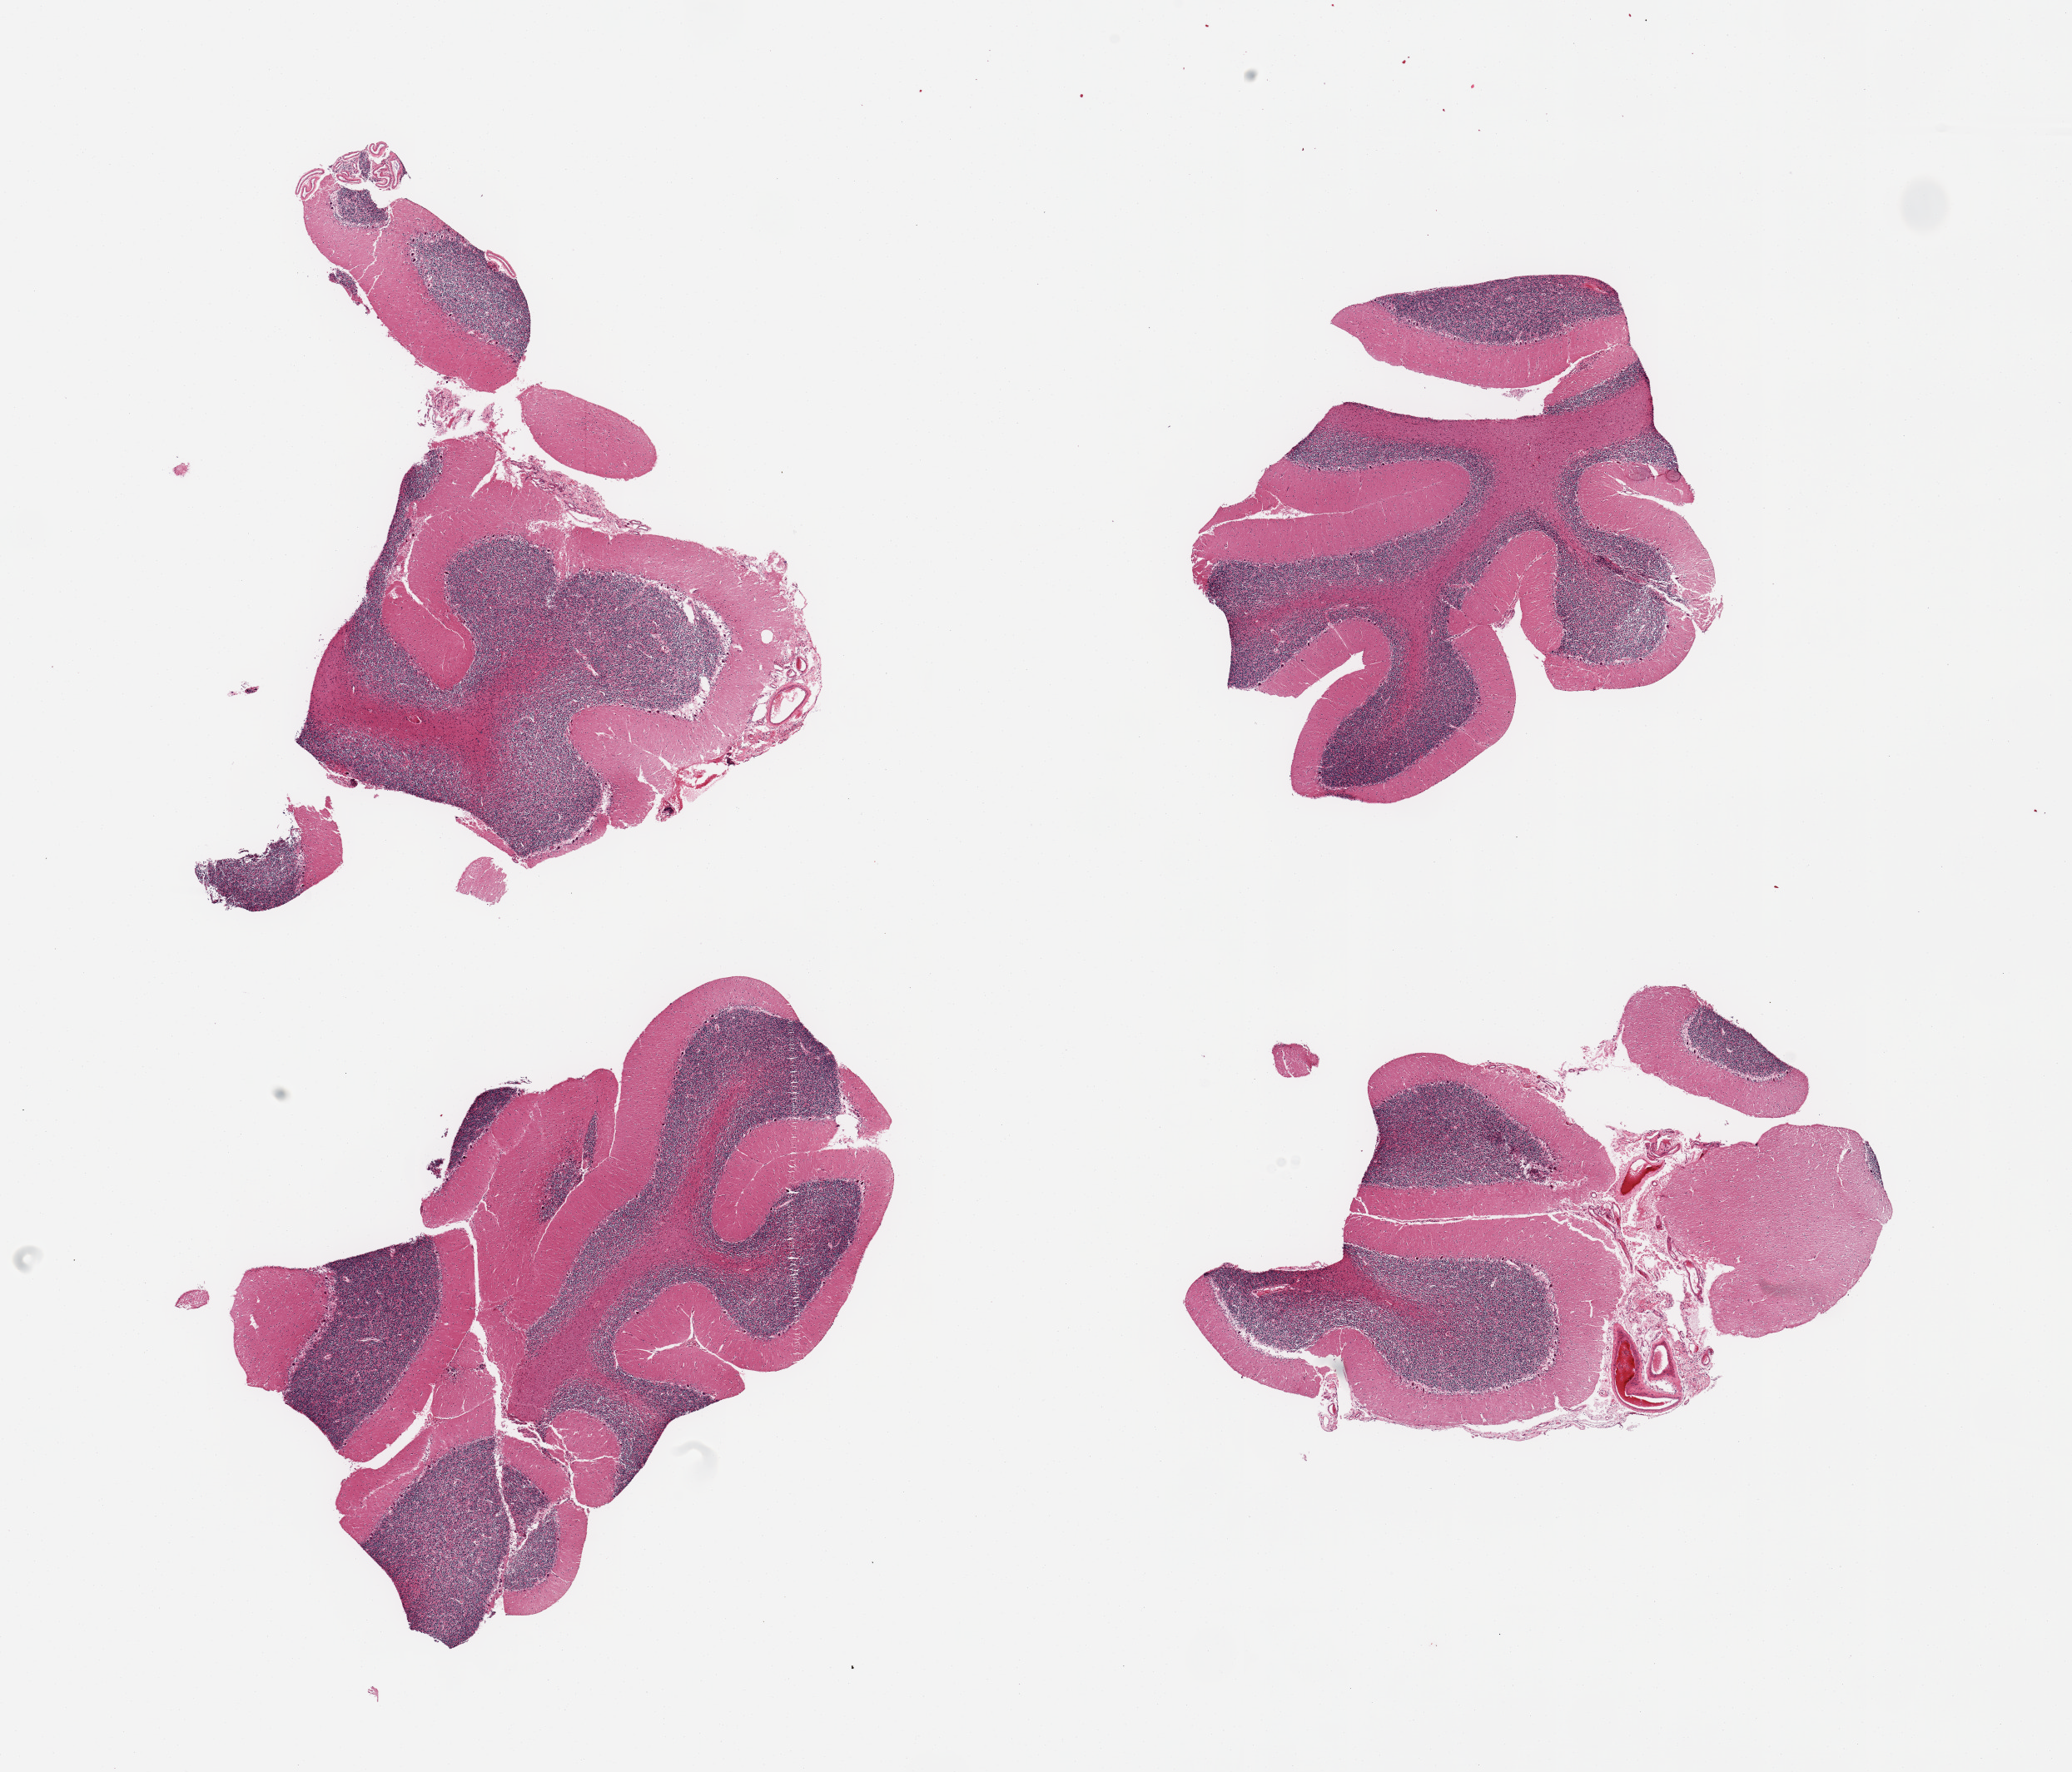
Whole-slide image, hematoxylin and eosin (H&E) stain, low-resolution overview of the scanned area, about 19.7 x 16.8 mm; PAXgene-fixed, paraffin-embedded tissue; sampled site (target tissue): cerebellum; tissue donor sample. Donor: male.
Reviewer comment on this tissue sample: 4 pieces, no abnormalities.